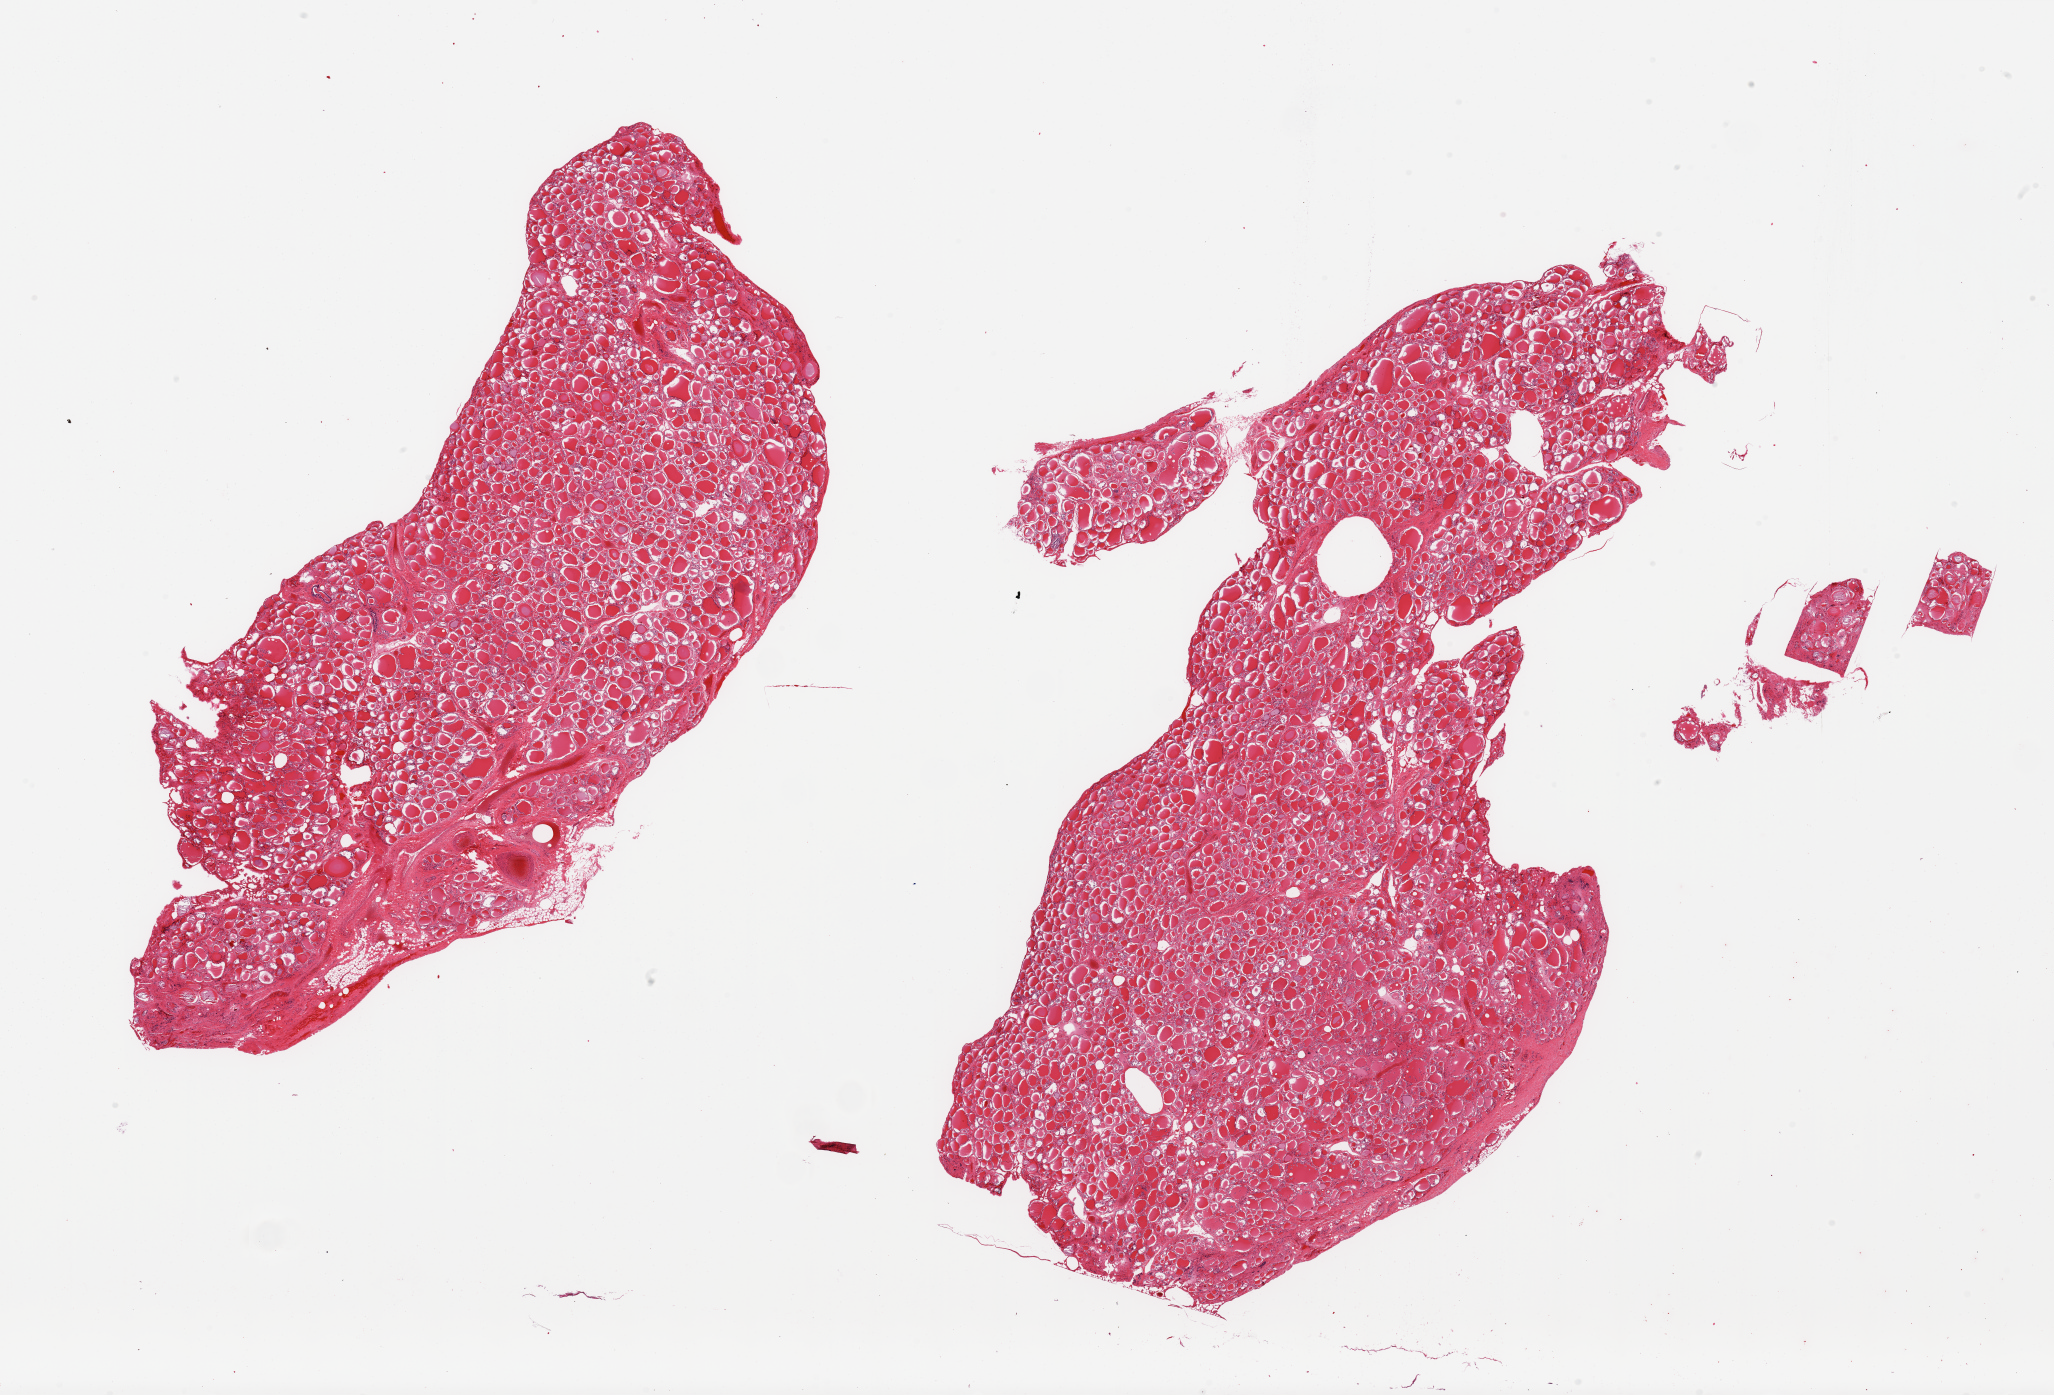
Digitized H&E-stained section, brightfield — whole scanned area (about 32.5 x 22.1 mm, from a 20x scan) shown as a low-resolution overview, PAXgene-fixed paraffin-embedded (PFPE) section, section of thyroid (target tissue), donor tissue sample. Donor sex: male.
• reviewer comment on this tissue sample: 2 pieces; <5% external fat